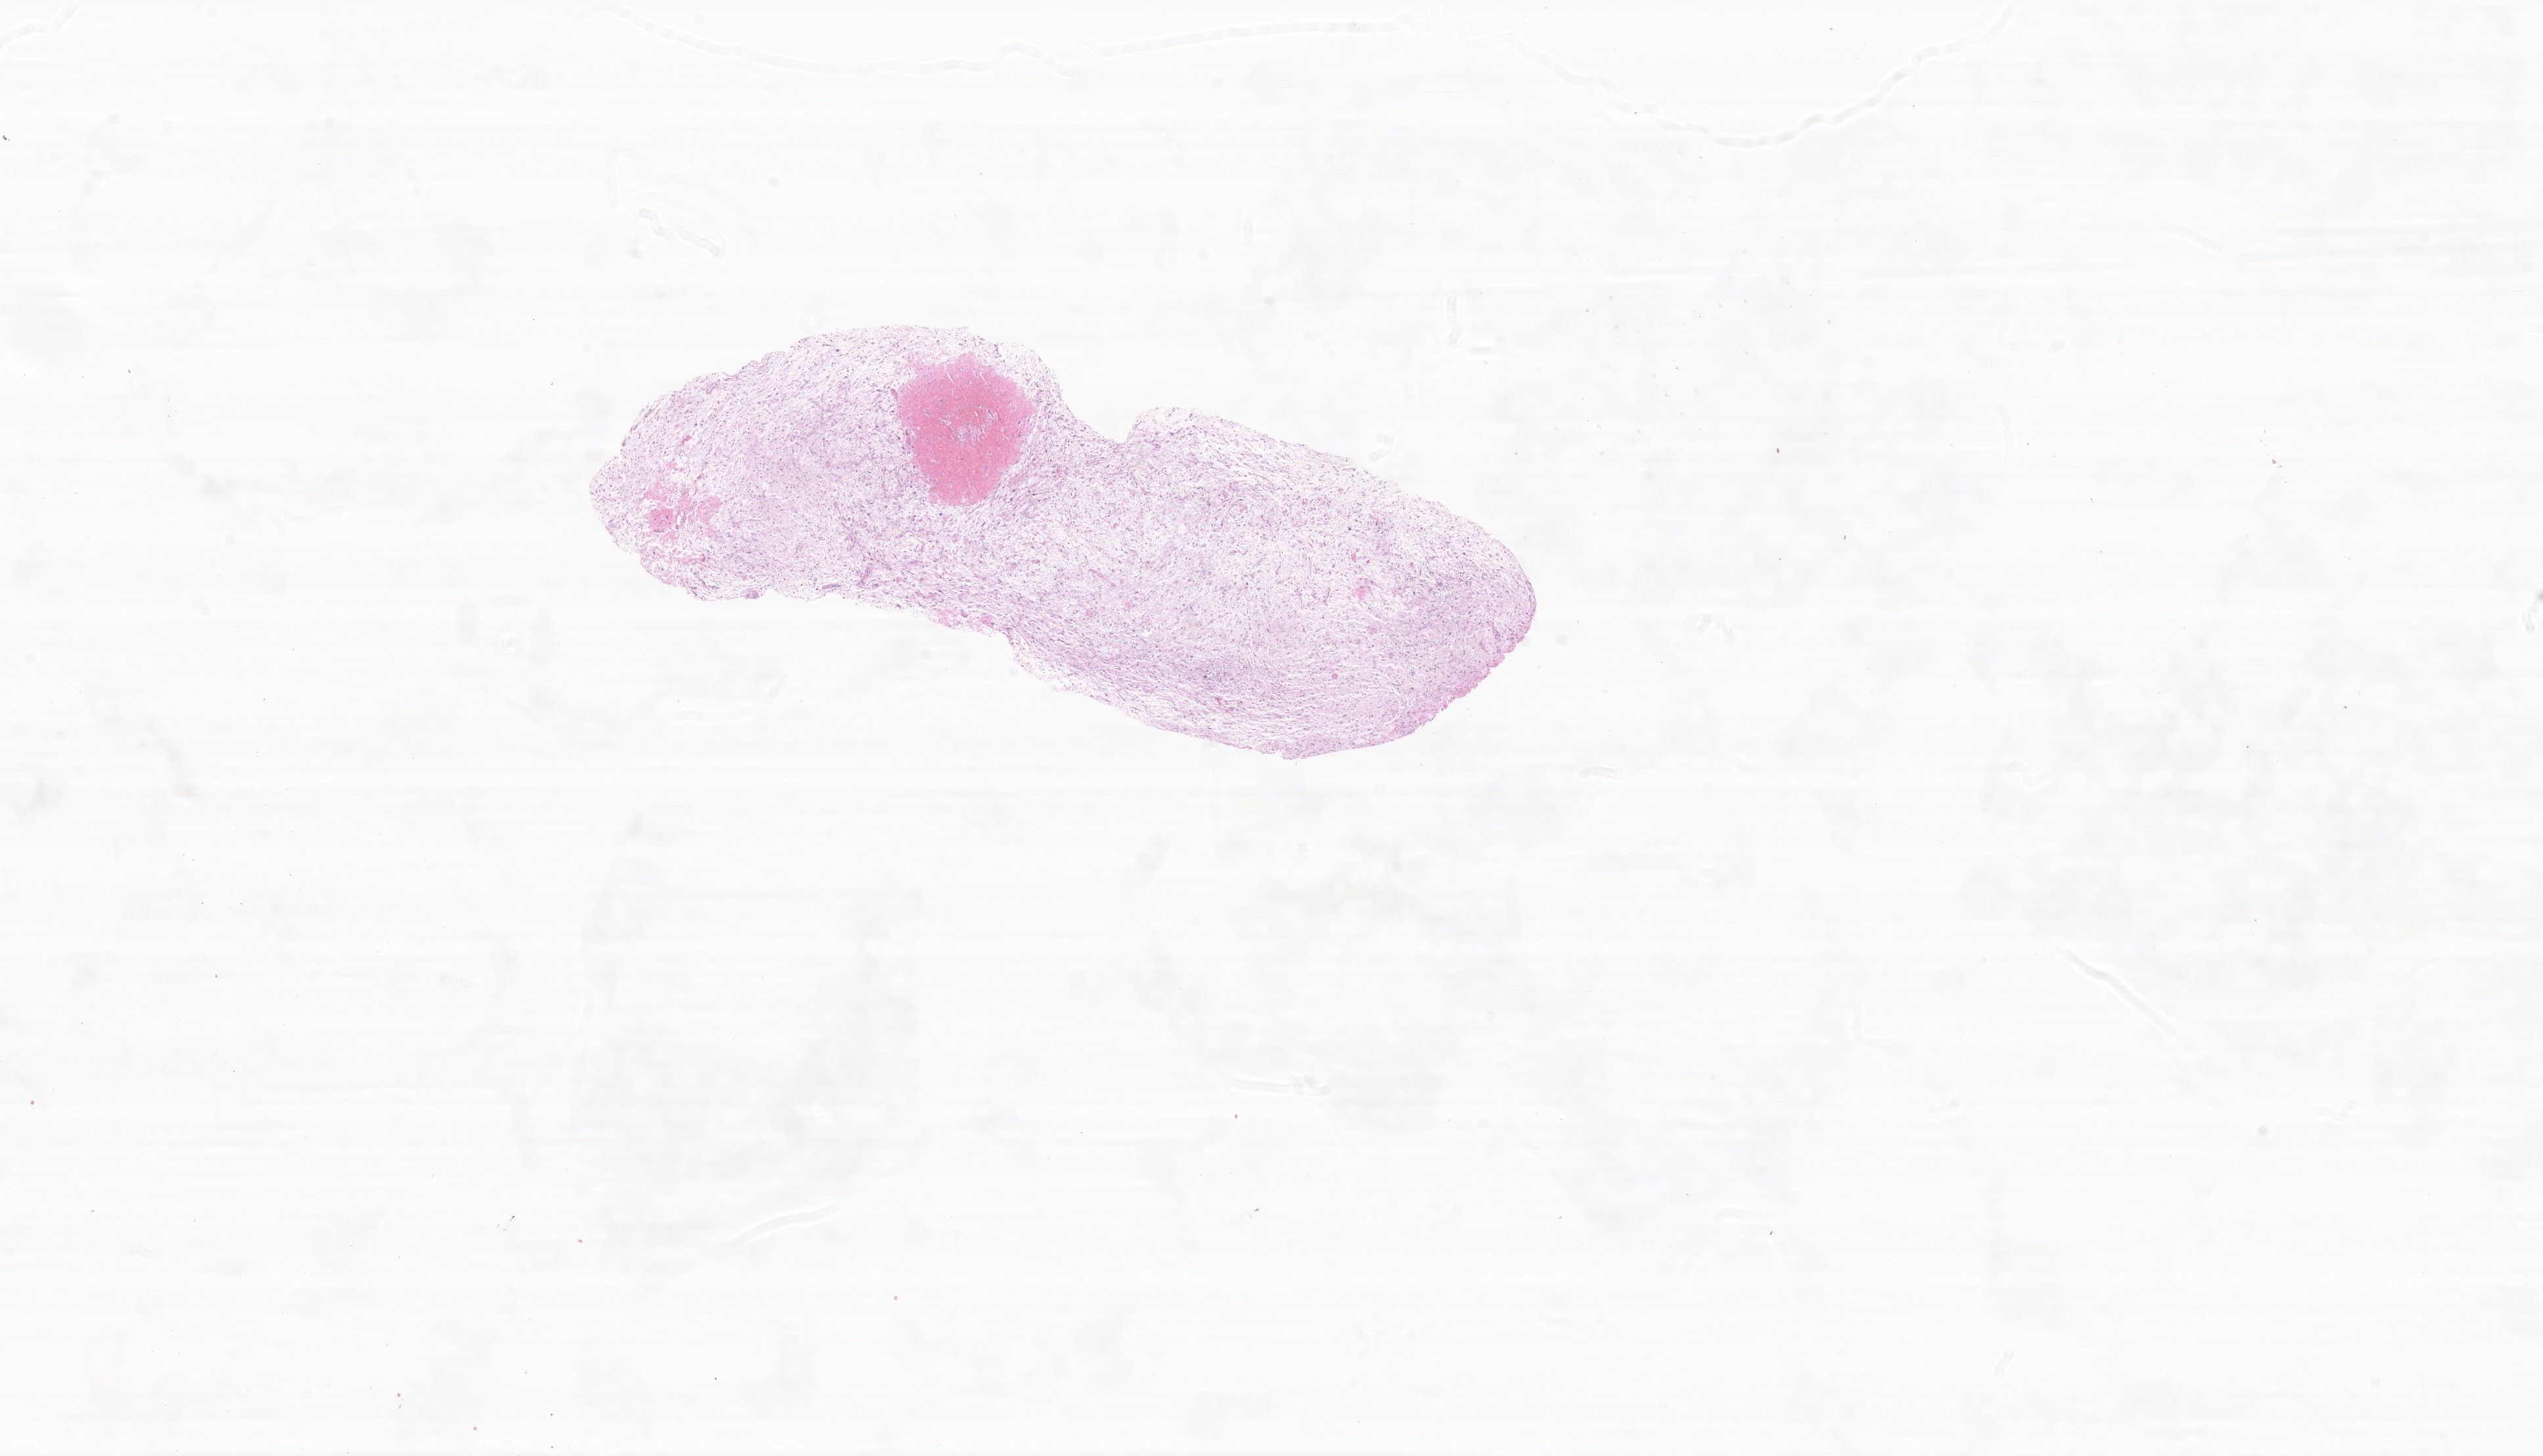
Whole-slide image, haematoxylin and eosin stain of tumor tissue from the brain, low-resolution overview of the scanned area, about 16.3 x 9.3 mm. Patient: female, age 116 months (9 years 8 months).
Specimen: formalin-fixed paraffin-embedded section.